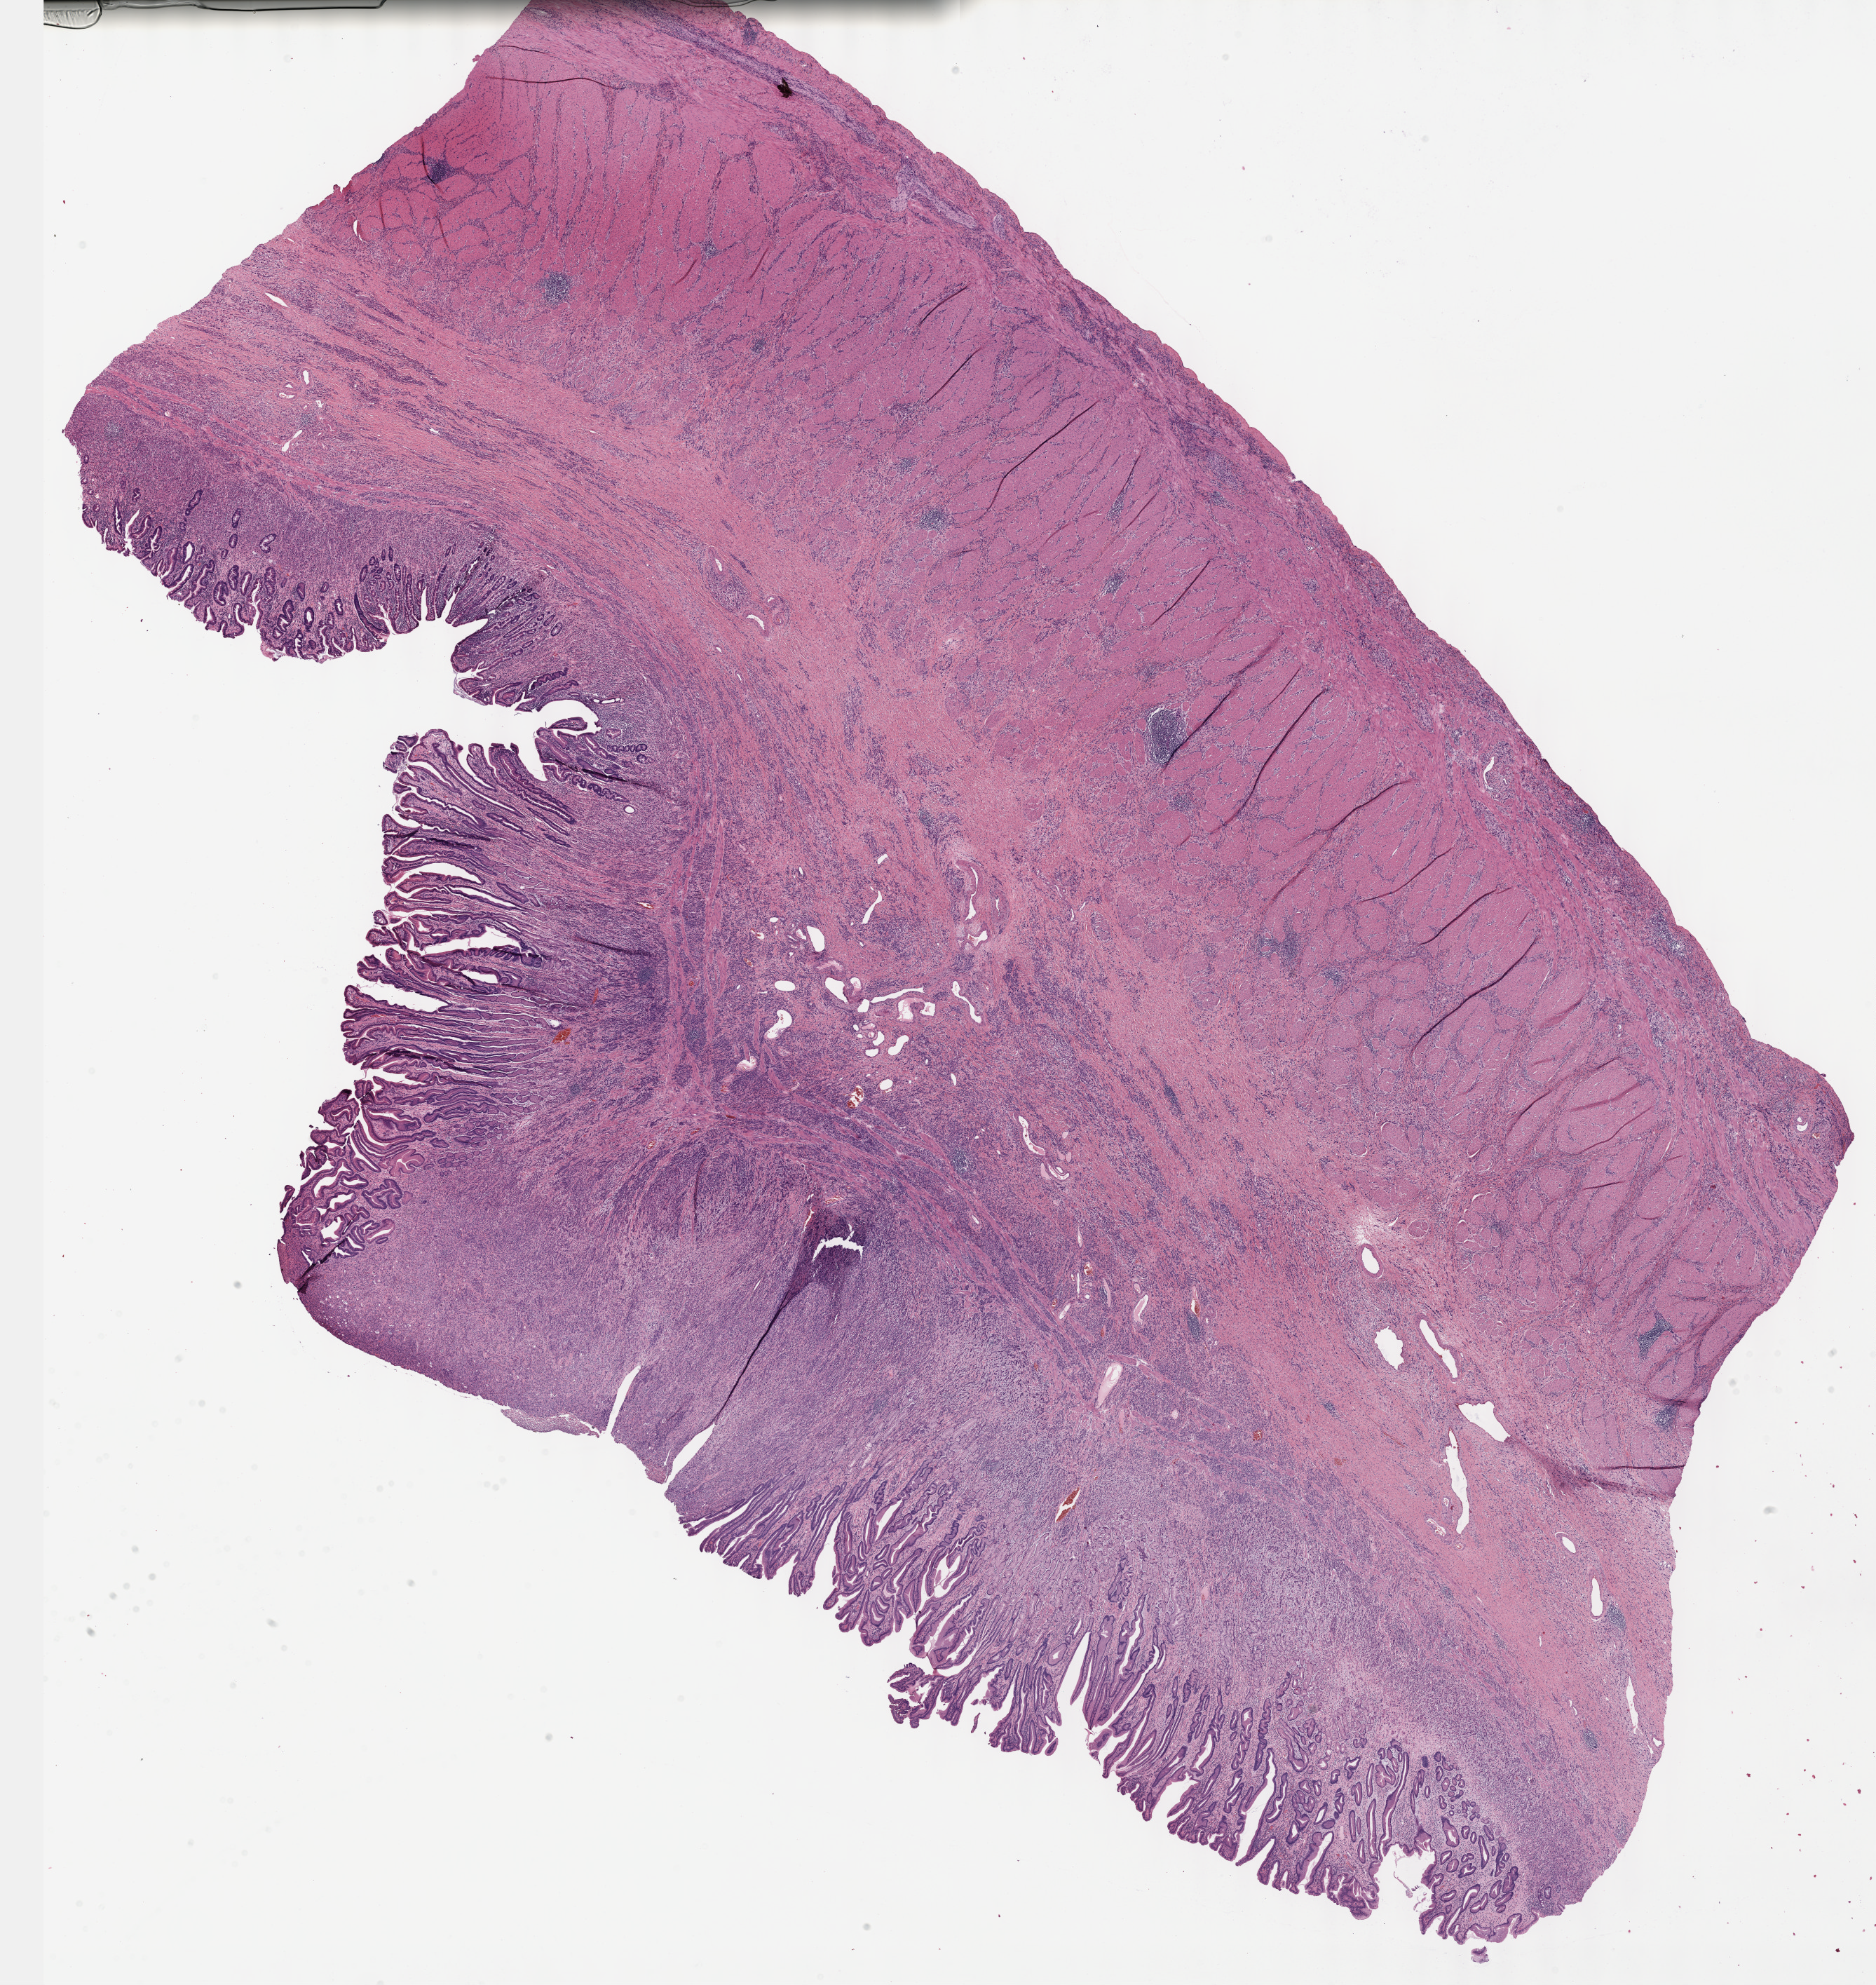
Whole-slide histology image, Hematoxylin and eosin (H&E) stained, whole scanned area (about 21.6 x 22.9 mm) shown as a low-resolution overview, formalin-fixed paraffin-embedded (FFPE) diagnostic section, primary tumour sample from the stomach. Patient: male, age at initial diagnosis 81 years.
Pathologic diagnosis: Carcinoma, diffuse type (body of stomach).